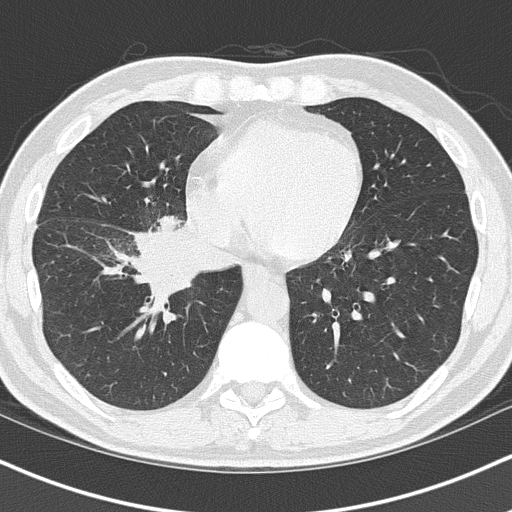
Low-dose screening chest CT, one axial slice; slice 47 of 151 in the series (ordered by position); reconstruction kernel B50f; lung window (W 1500 / L -600 HU); 2 mm slice thickness; 512 × 512 image matrix.
Structures marked on this image (manually delineated by an expert):
- lesion 1 (tumor, hilum of right lung): bounding box (x1, y1, x2, y2) in pixels: (132, 217, 195, 296)